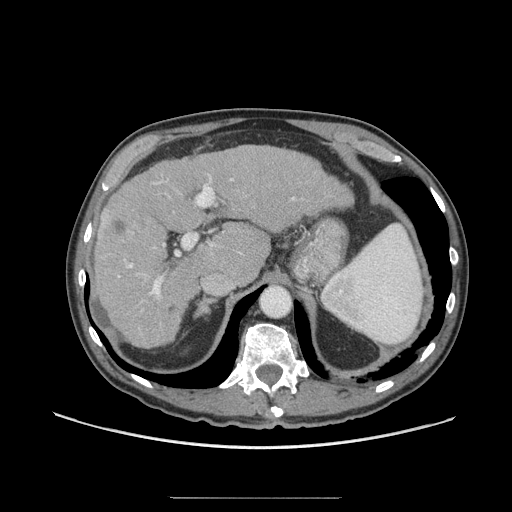
Contrast-enhanced abdominal CT (liver protocol), one axial slice; position 46 of 71 along the scan axis; soft-tissue window (W 400 / L 40 HU); 2.5 mm slice thickness; 512 × 512 image matrix, field of view 400 × 400 mm. Case-level facts recorded for this patient, not image findings: diagnosis: hepatocellular carcinoma (patient treated with transarterial chemoembolisation; whether this scan precedes or follows treatment is not stated here); TNM stage (as recorded): Stage-I; Child-Pugh class: A; tumour nodularity: uninodular; tumour size: 3.5 cm.
Annotated regions visible in this slice (semi-automatically segmented with operator editing):
- liver parenchyma outside the tumour (the mass and vessels are separate outlines, so this box may not span the whole liver): bounding box <92,144,344,346> (left, top, right, bottom; pixels)
- mass: <100,207,133,246>
- liver vessels: <118,174,295,299>